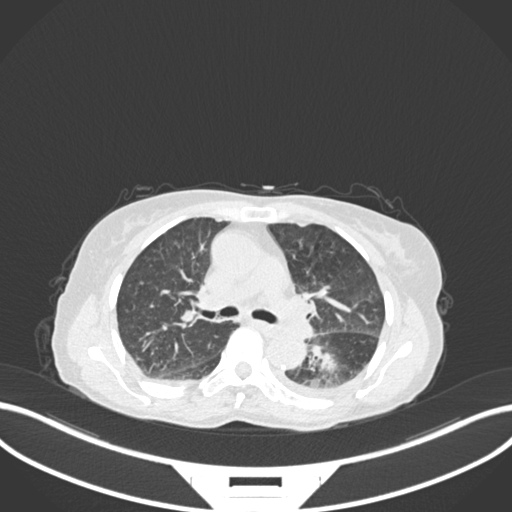
Chest CT, one axial slice. Position 110 of 233 along the scan axis. 120 kVp. Lung window (W 1500 / L -600 HU). 512 × 512 image matrix, field of view 400 × 400 mm. Patient: female, 78 years. From the clinical record (not read from this slice): clinical TNM (as recorded): T3 N0 M1.
Structures marked on this image (bounding box drawn by a radiologist):
- lung tumour (recorded histology: squamous cell carcinoma): bounding box <301,332,355,389> (left, top, right, bottom; pixels)